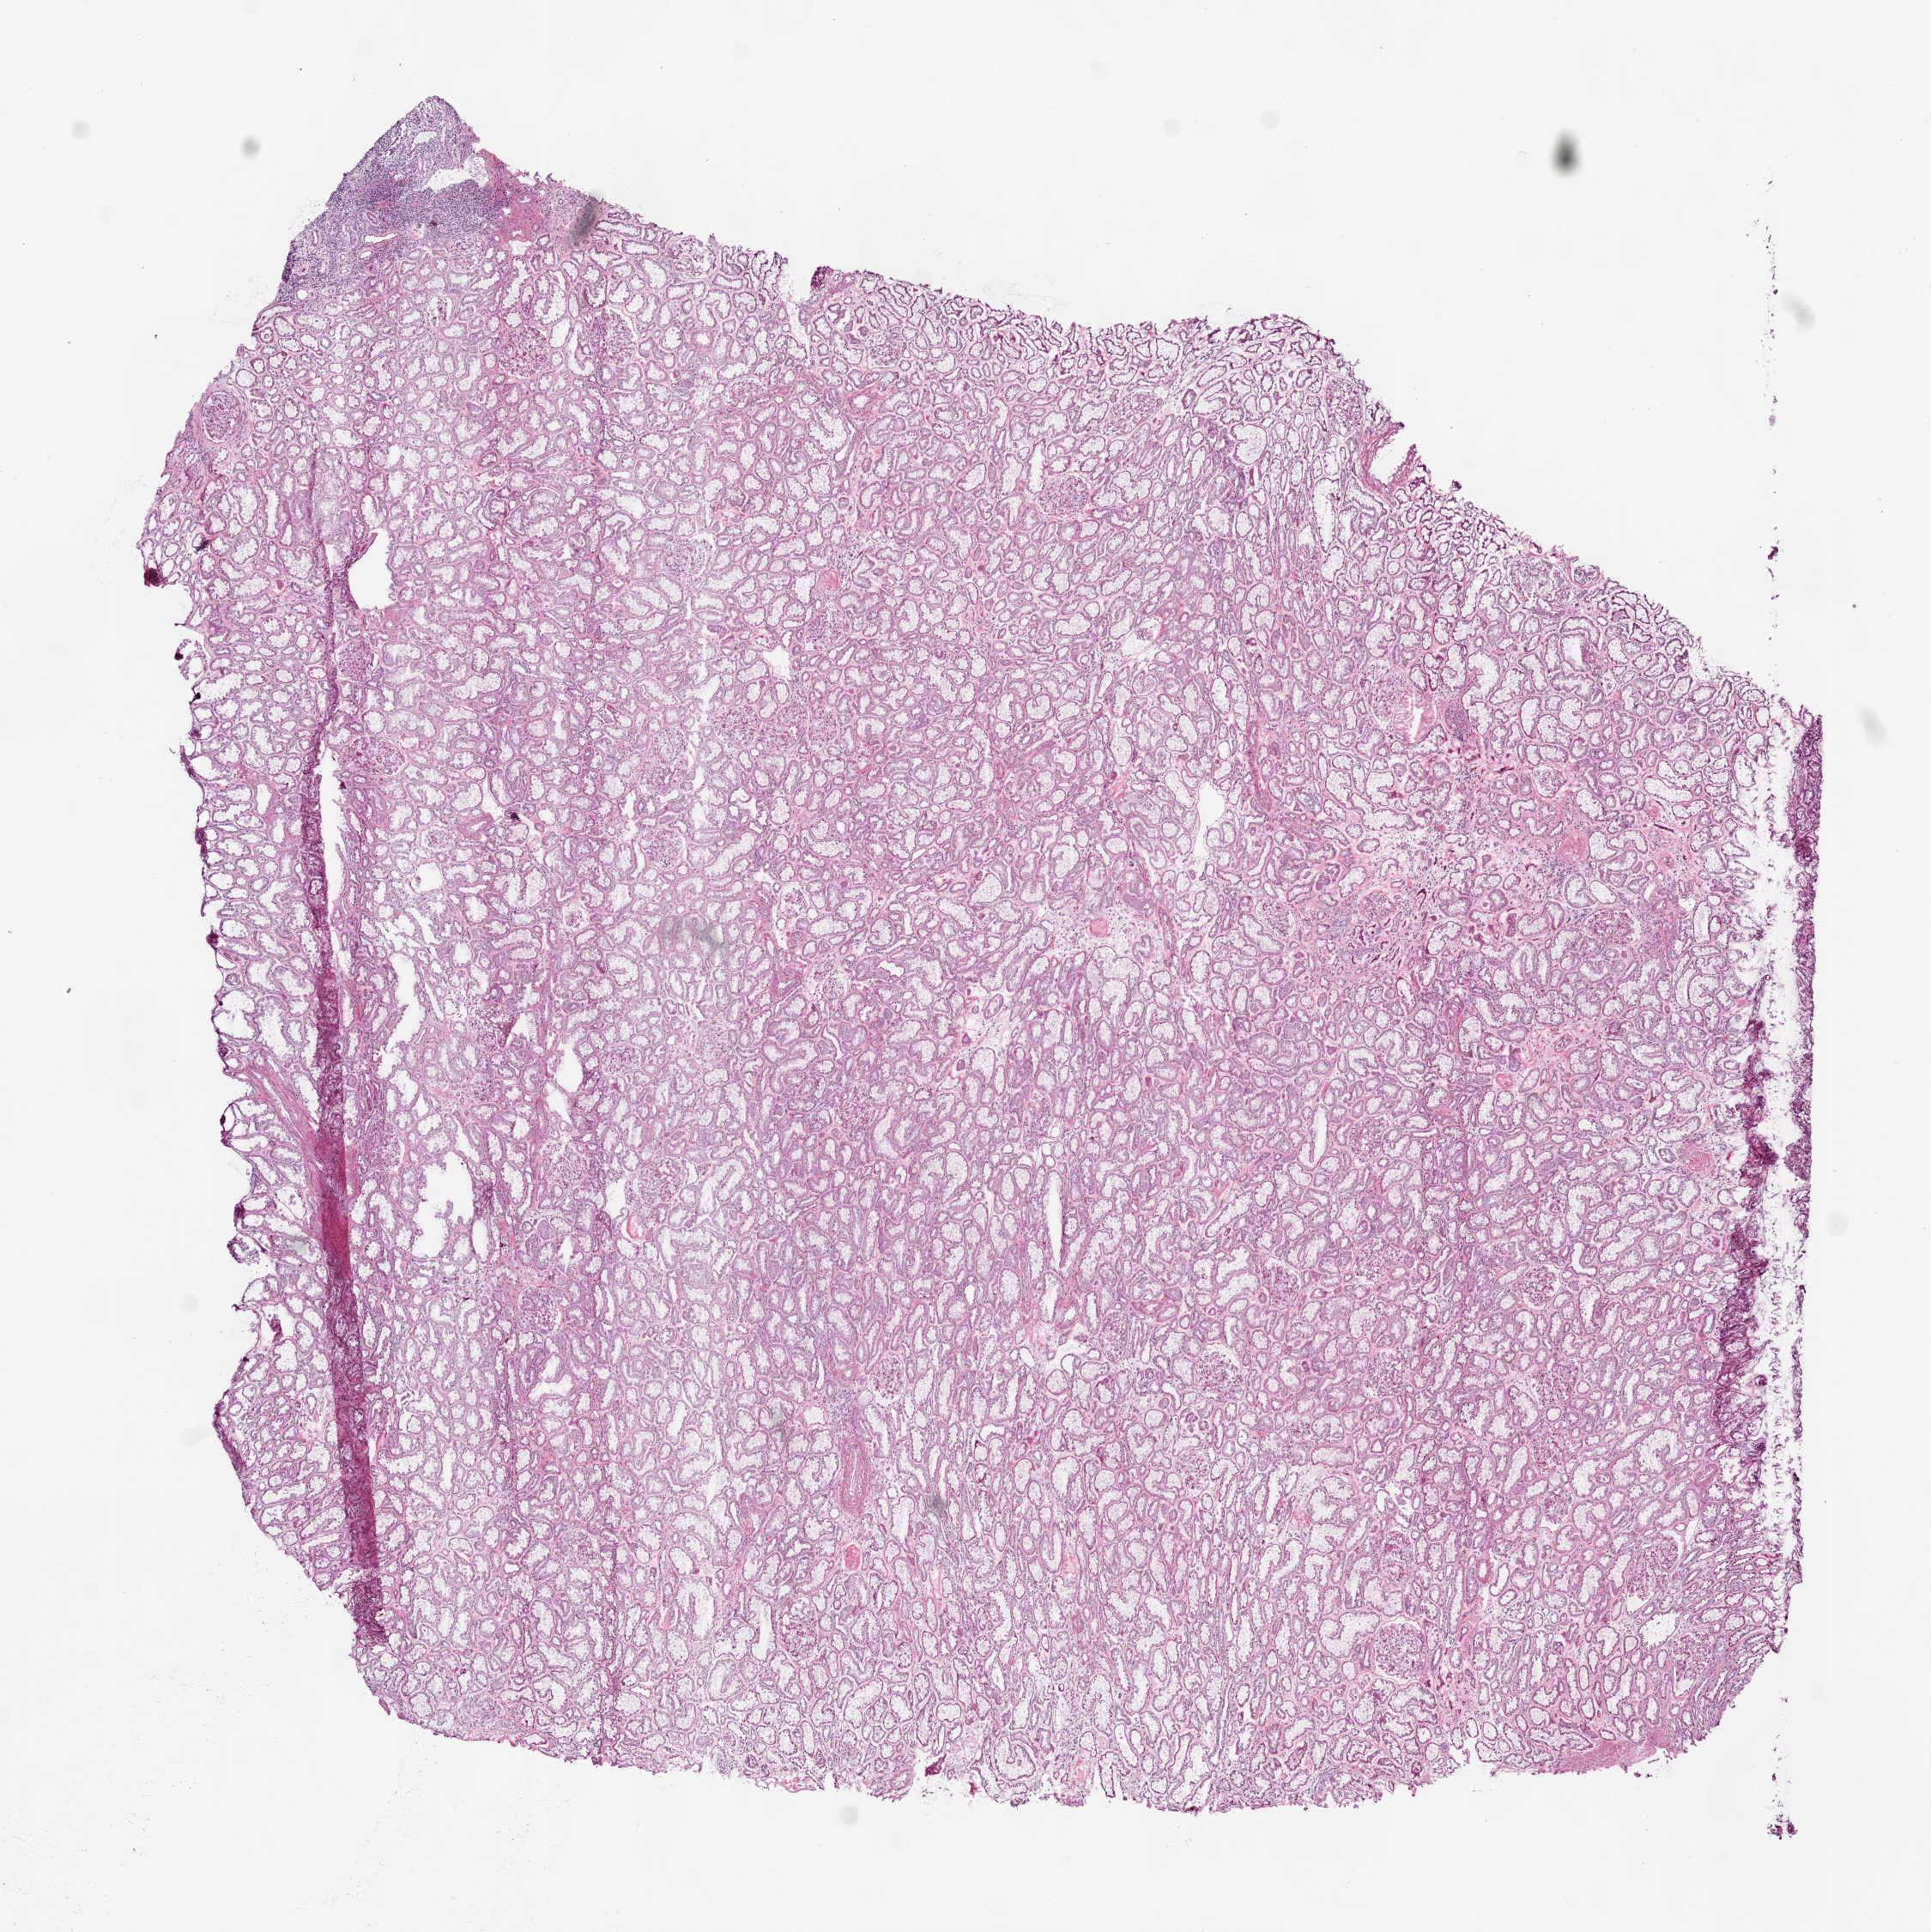
Digitized H&E tissue section (whole slide), whole scanned area (about 9.0 x 9.0 mm) shown as a low-resolution overview, frozen section from the bottom of the tissue portion, sample: solid tissue normal (non-tumour tissue), kidney. Male, age 64 years at initial diagnosis.
- this section: solid tissue normal sample (biorepository sample class)
- patient diagnosis: Papillary adenocarcinoma, NOS